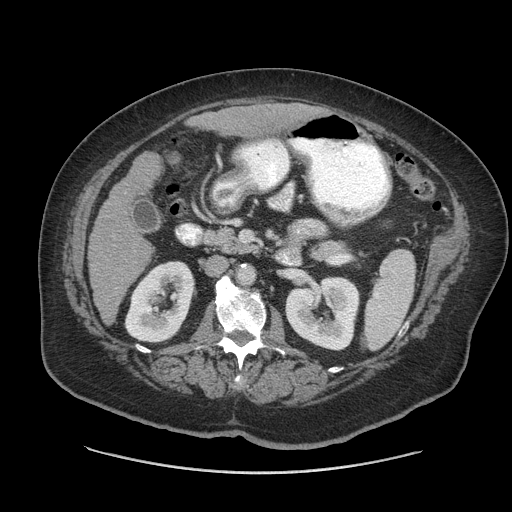
Contrast-enhanced abdominal CT (liver protocol), one axial slice; slice 24 of 91 in the series (ordered by position); reconstruction kernel STANDARD; soft-tissue window (W 400 / L 40 HU); 2.5 mm slice thickness; 512 × 512 image matrix, field of view 420 × 420 mm. Case-level facts recorded for this patient, not image findings: diagnosis: hepatocellular carcinoma (patient treated with transarterial chemoembolisation; whether this scan precedes or follows treatment is not stated here); TNM stage (as recorded): Stage-I; Child-Pugh class: A; tumour nodularity: uninodular.
Structures marked on this image (semi-automatically segmented with operator editing):
- liver parenchyma outside the tumour (the mass and vessels are separate outlines, so this box may not span the whole liver): bounding box (x1, y1, x2, y2) in pixels: (88, 104, 313, 322)